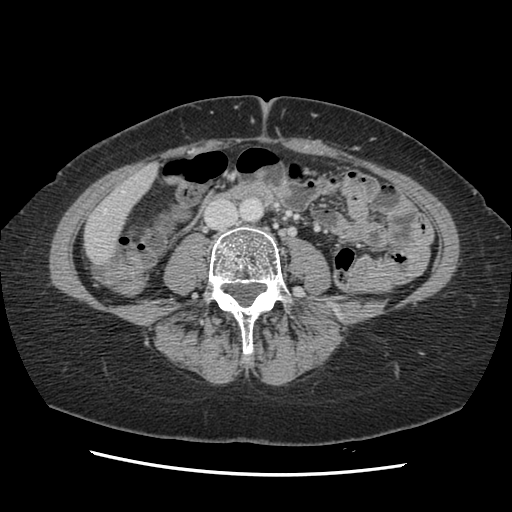
Contrast-enhanced abdominal CT, one axial slice. Position 22 of 141 along the scan axis. Soft-tissue window (W 400 / L 40 HU). 512 × 512 image matrix, field of view 330 × 330 mm. Female patient, age 61 years. Case-level facts recorded for this patient, not image findings: diagnosis: colorectal cancer liver metastases, imaged before liver resection; multiple liver metastases: no; largest metastasis: 2.4 cm.
Annotated regions visible in this slice (outlined manually by an expert reader):
- hepatic veins: bounding box (x1, y1, x2, y2) in pixels: (95, 210, 106, 241)
- liver: (85, 166, 157, 262)
- planned liver remnant (the part of the liver to remain after resection): (85, 167, 157, 262)